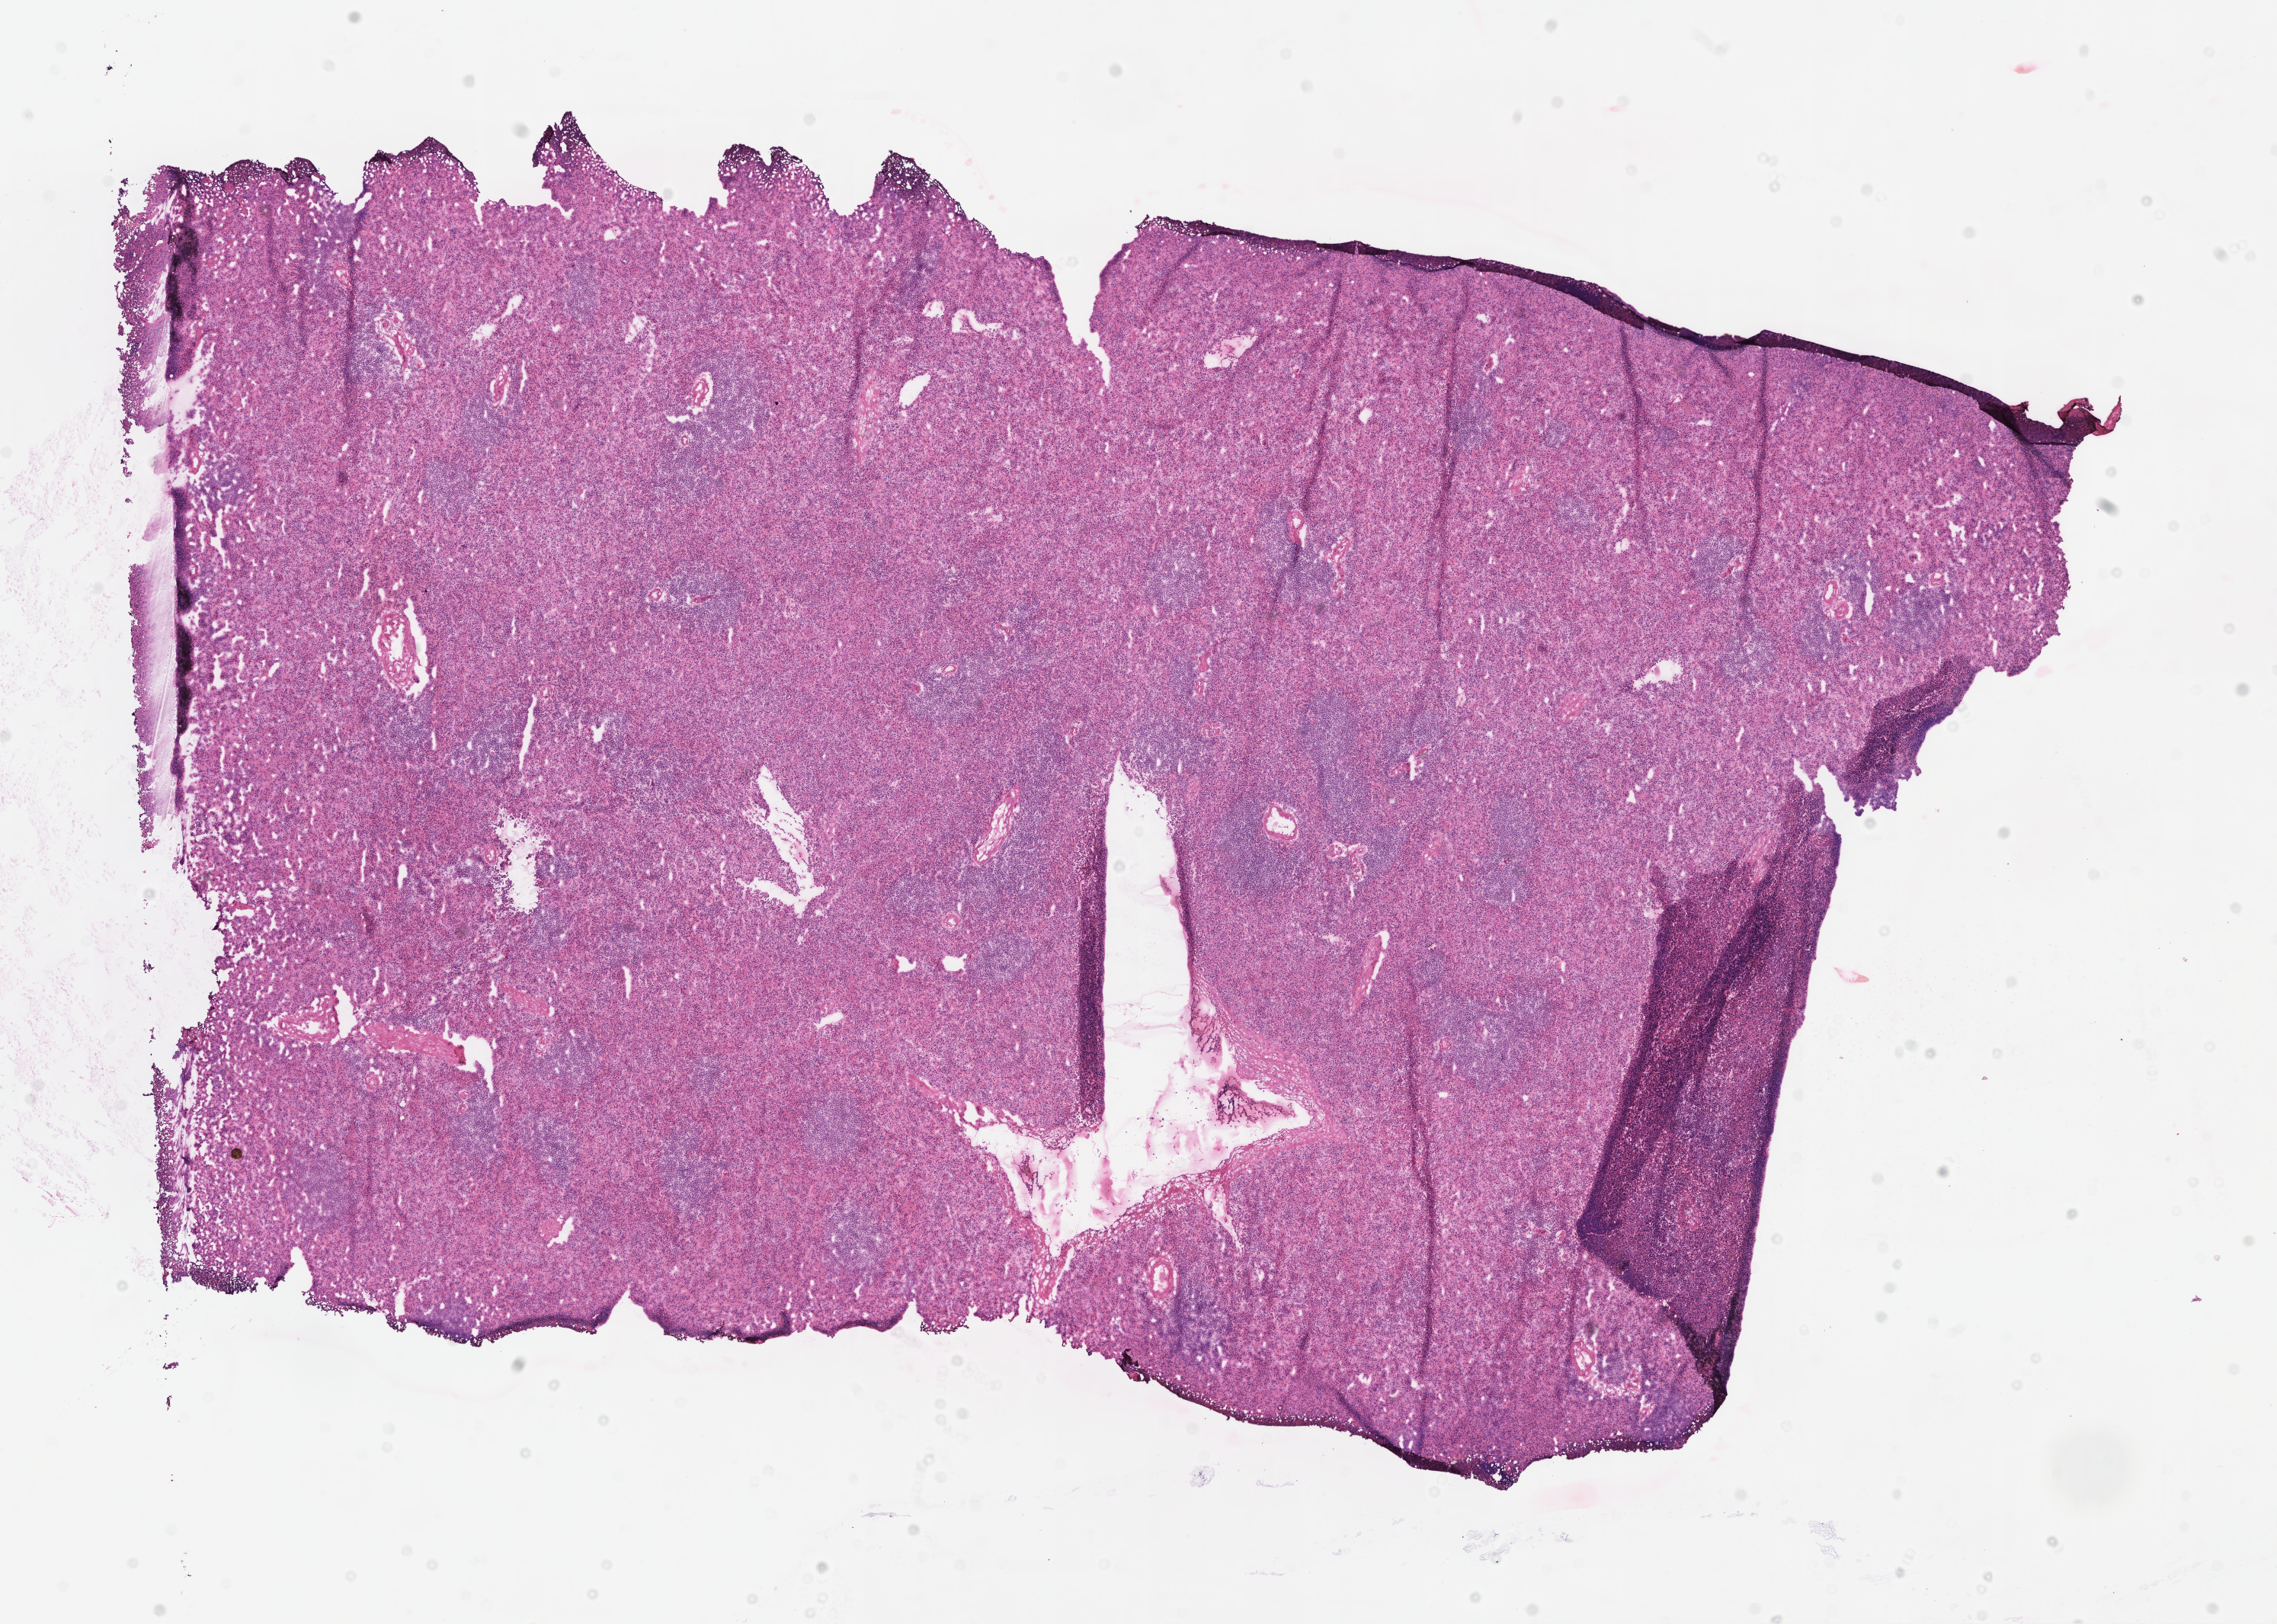
Whole-slide image, H&E stain — shown as a low-resolution overview of the whole scanned area (about 12.1 x 8.6 mm); frozen section; non-tumor (normal tissue) sample from a patient with intraductal papillary mucinous neoplasm with invasive carcinoma; site: head of pancreas. Male, age 77 years at initial diagnosis. Composition of this section per pathologist review: tumor cells 0%, tumor nuclei 0%, stromal cells 0%, necrosis 0%, normal cells 100%. Inflammatory infiltration, as recorded: lymphocyte infiltration 0%, monocyte infiltration 0%, neutrophil infiltration 0%.
This section: non-tumor tissue sample; the patient's diagnosis is given above. Section: top of the tissue portion.